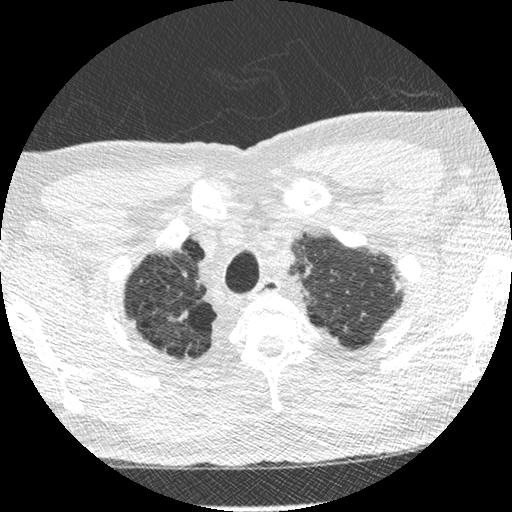
Low-dose screening chest CT, one axial slice. Slice 249 of 275 in the series (ordered by position). Reconstruction kernel STANDARD. 120 kVp. Lung window (W 1500 / L -600 HU). 1.25 mm slice thickness. 512 × 512 image matrix.
Structures marked on this image (manually delineated by an expert):
- lesion 1 (tumor, upper lobe of left lung): bounding box <392,275,401,293> (left, top, right, bottom; pixels)